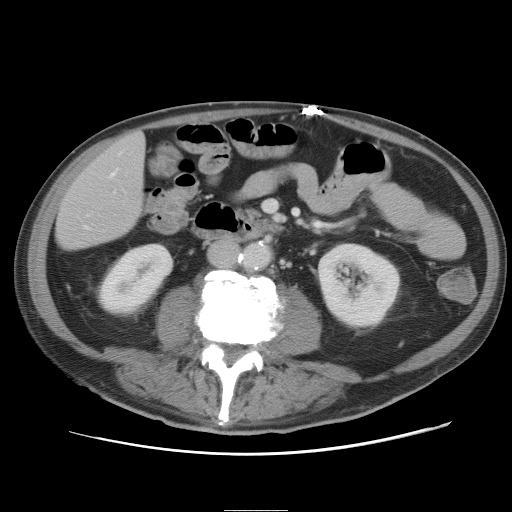
Contrast-enhanced abdominal CT, one axial slice; slice 11 of 89 in the series (ordered by position); 120 kVp; soft-tissue window (W 400 / L 40 HU); 5 mm slice thickness; 512 × 512 image matrix, field of view 375 × 375 mm. Male patient, age 69 years. From the clinical record (not read from this slice): diagnosis: colorectal cancer liver metastases, imaged before liver resection; multiple liver metastases: no; largest metastasis: 8.5 cm; disease in both lobes: no.
Annotated regions visible in this slice (manually delineated by an expert):
- hepatic veins: bounding box [x1, y1, x2, y2] px = [87, 169, 118, 228]
- liver: [57, 133, 145, 250]
- planned liver remnant (the part of the liver to remain after resection): [57, 133, 145, 250]